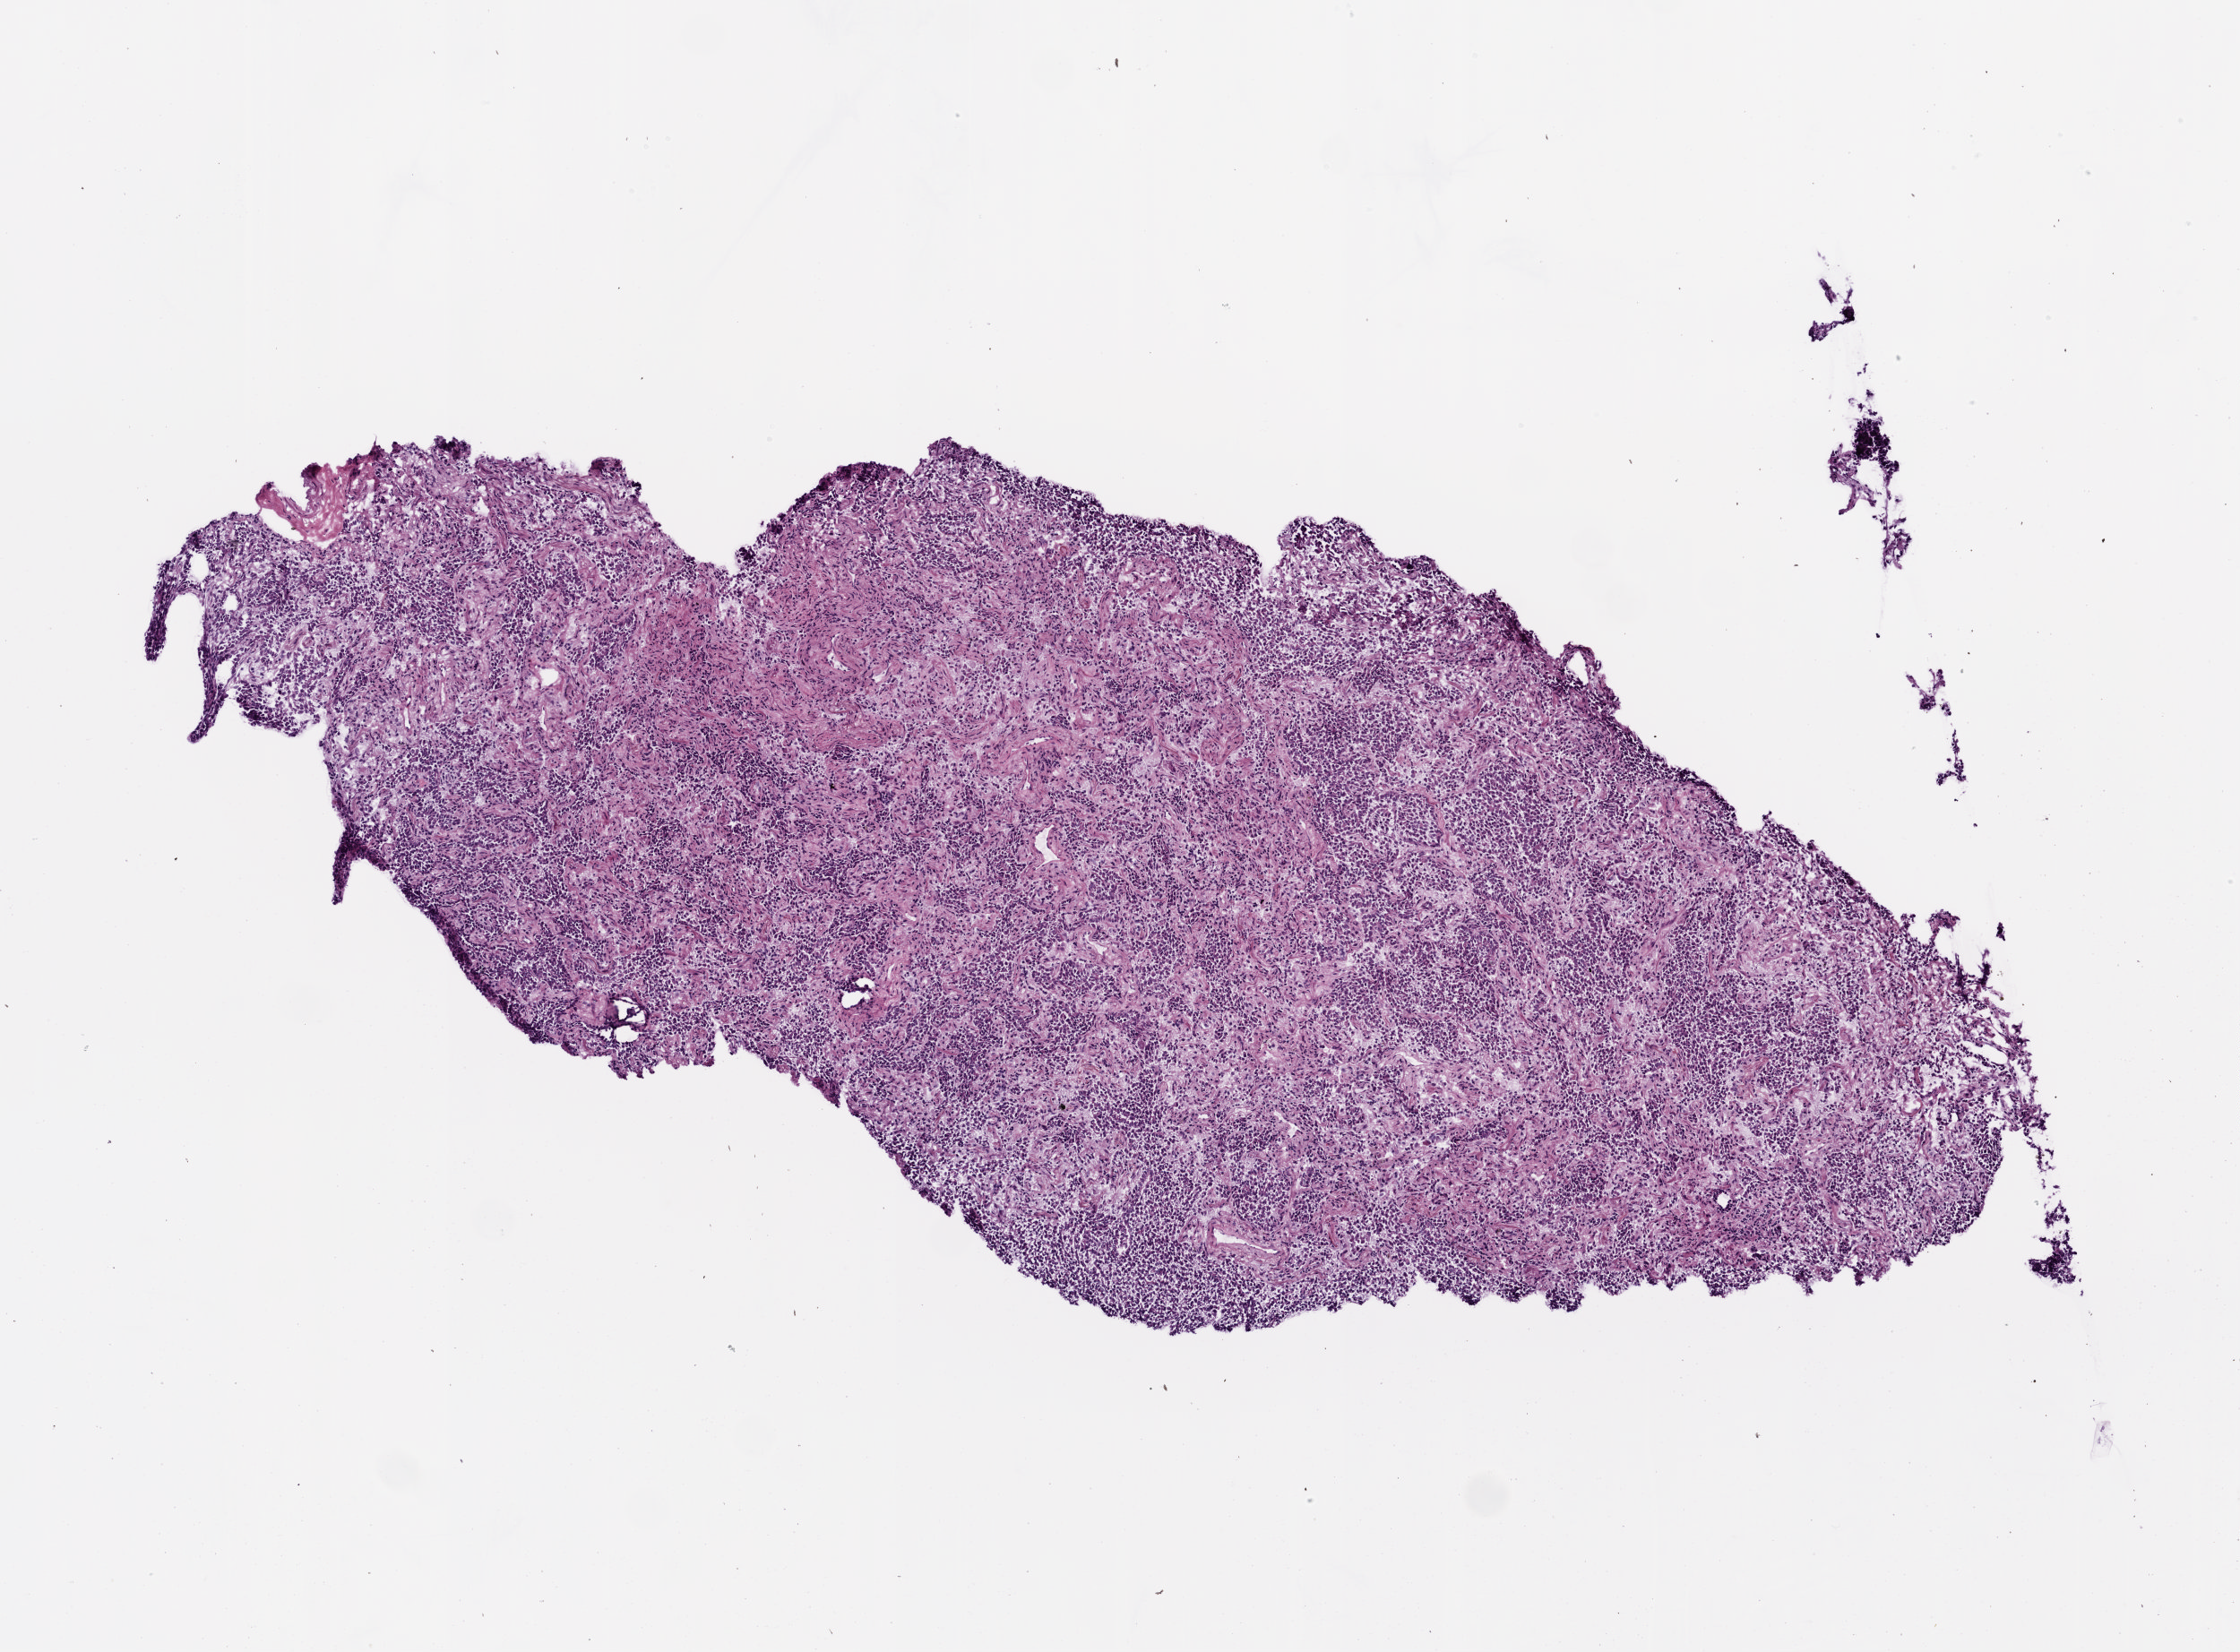
Digitized H&E-stained tissue section (whole slide) — low-resolution overview of the scanned area, about 5.0 x 3.7 mm (from a 20x scan), frozen section from the top of the tissue portion, primary tumour sample from the lung. Male patient; age at initial diagnosis 68 years. Slide review estimates, as recorded: tumour cells 85%, tumour nuclei 75%, normal cells 0%, stromal cells 15%, necrosis 0%.
- histologic diagnosis: Adenocarcinoma, NOS (lower lobe, lung)